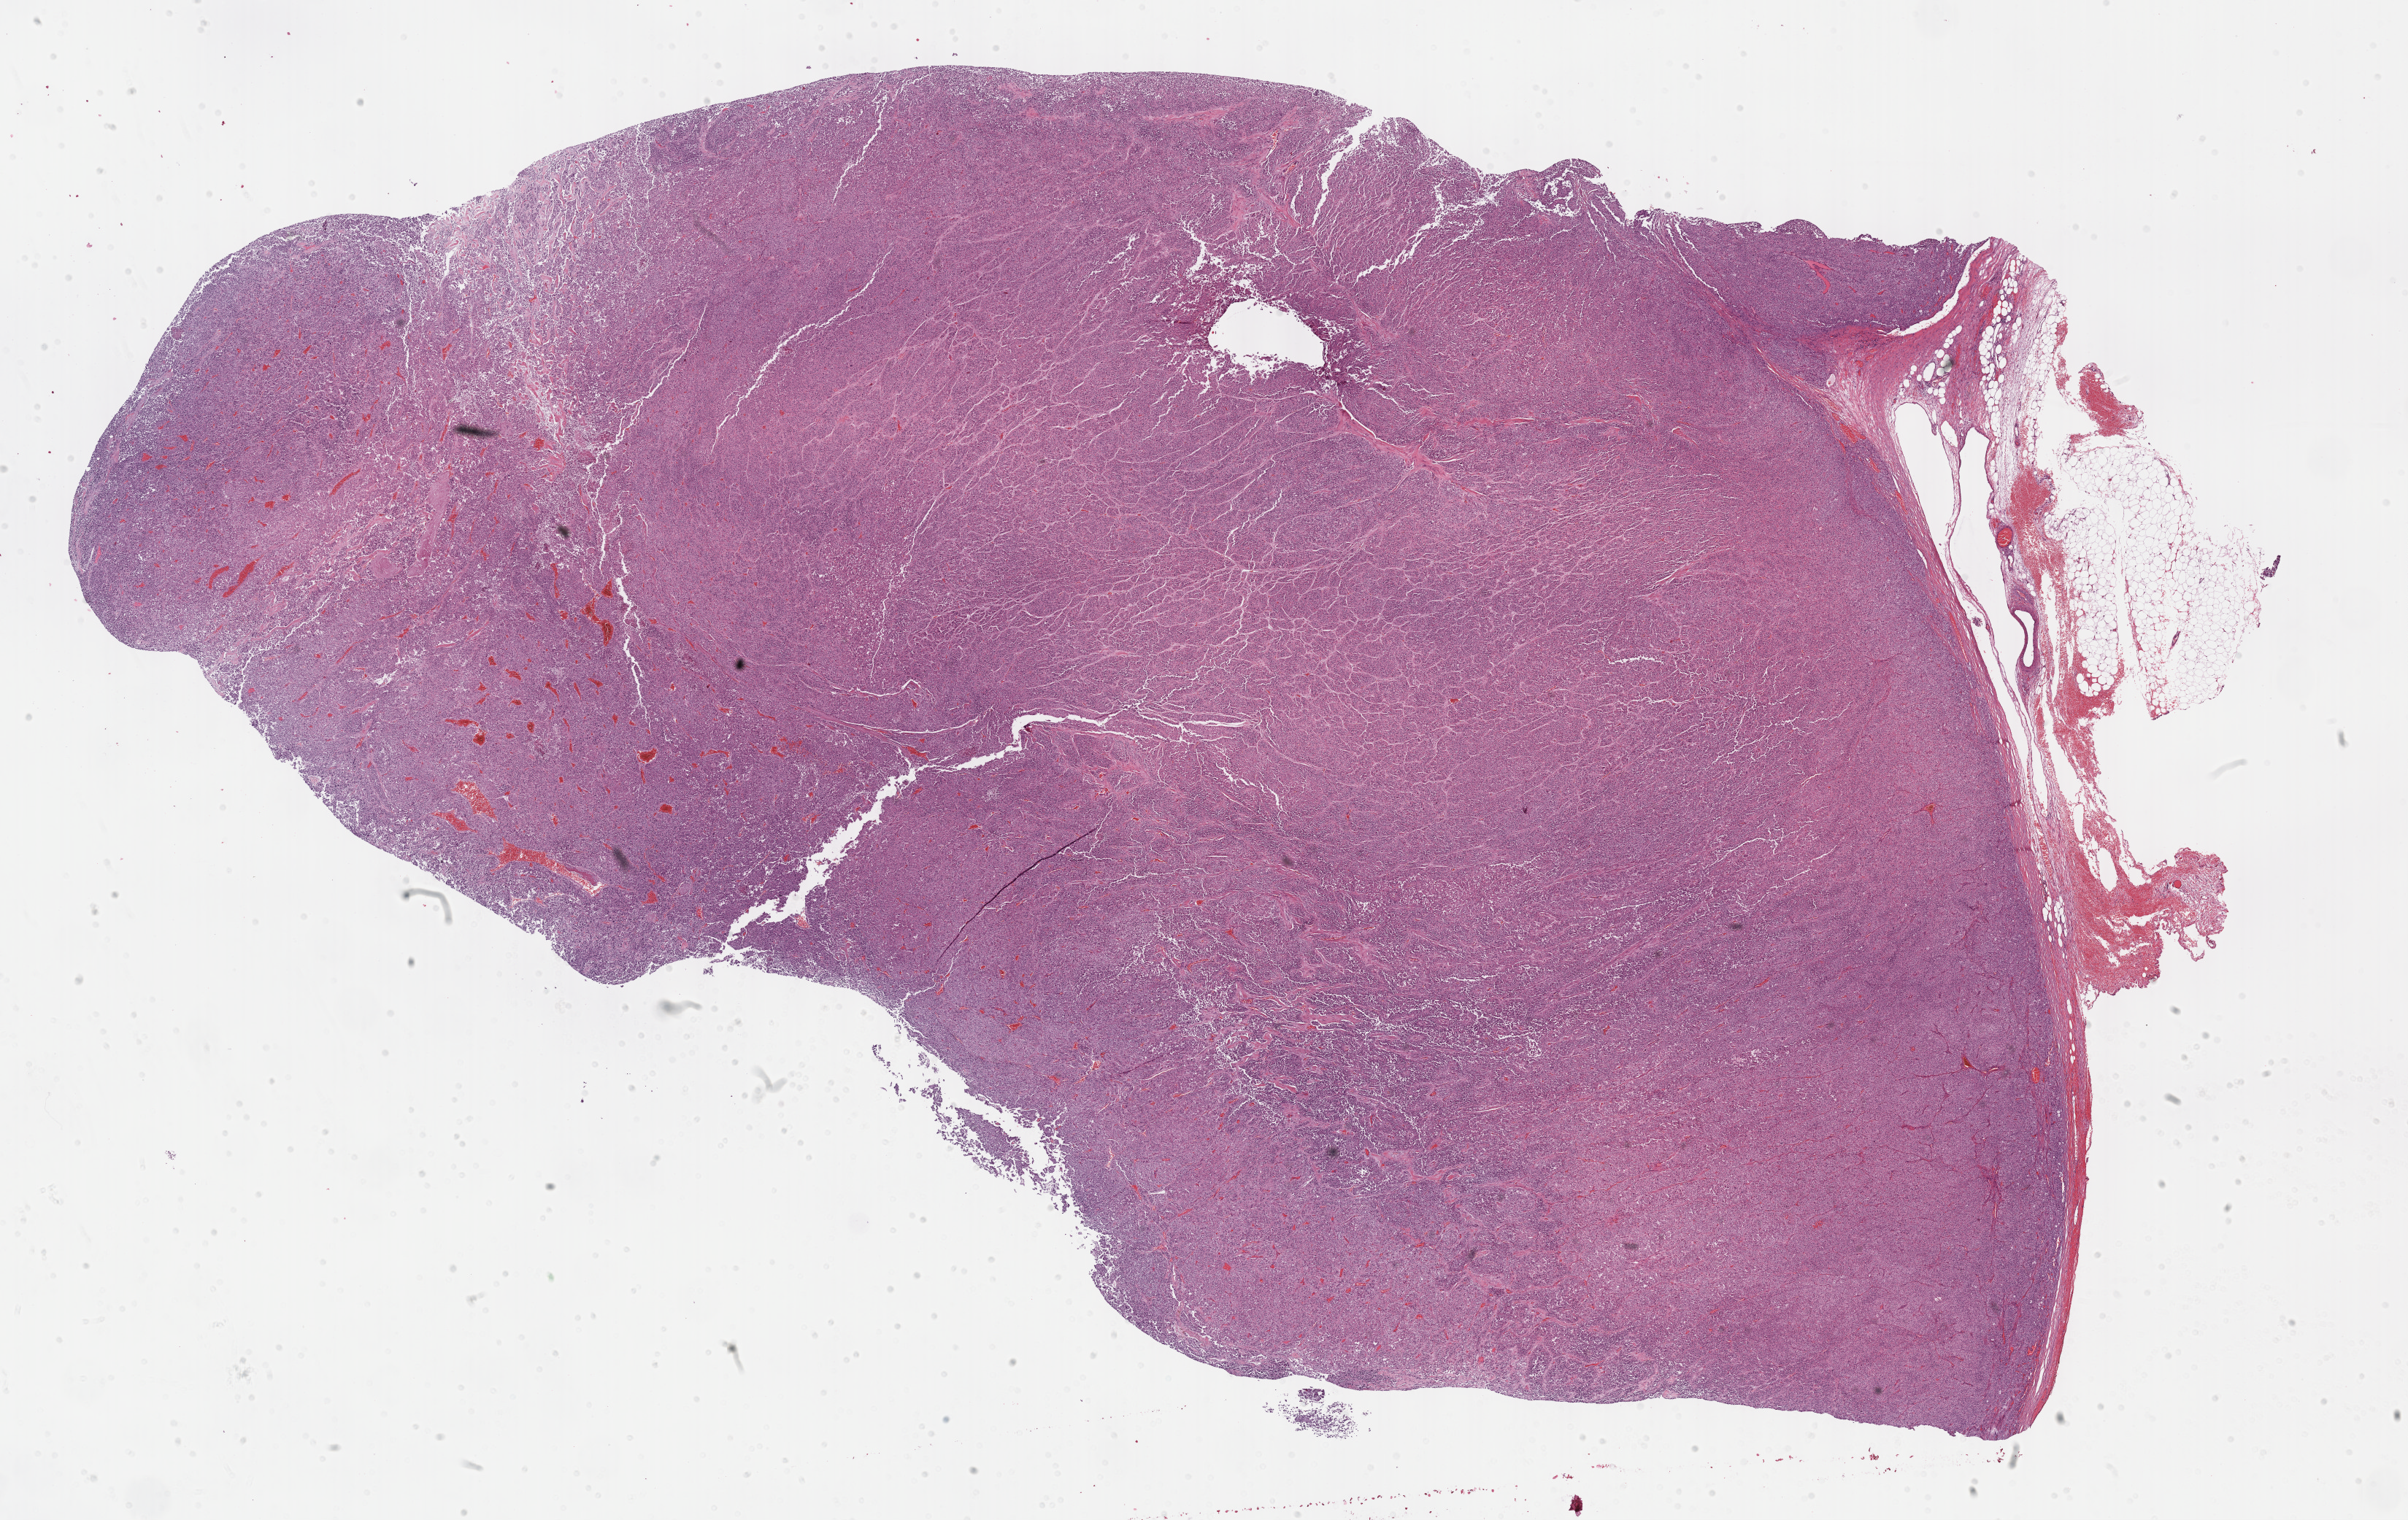
Whole-slide histology image, H&E-stained, whole scanned area (about 26.7 x 16.8 mm) shown as a low-resolution overview; formalin-fixed paraffin-embedded (FFPE) diagnostic section; primary tumour sample from the adrenal cortex. Male patient; age at initial diagnosis 39 years.
Diagnosis: Adrenal cortical carcinoma (cortex of adrenal gland).